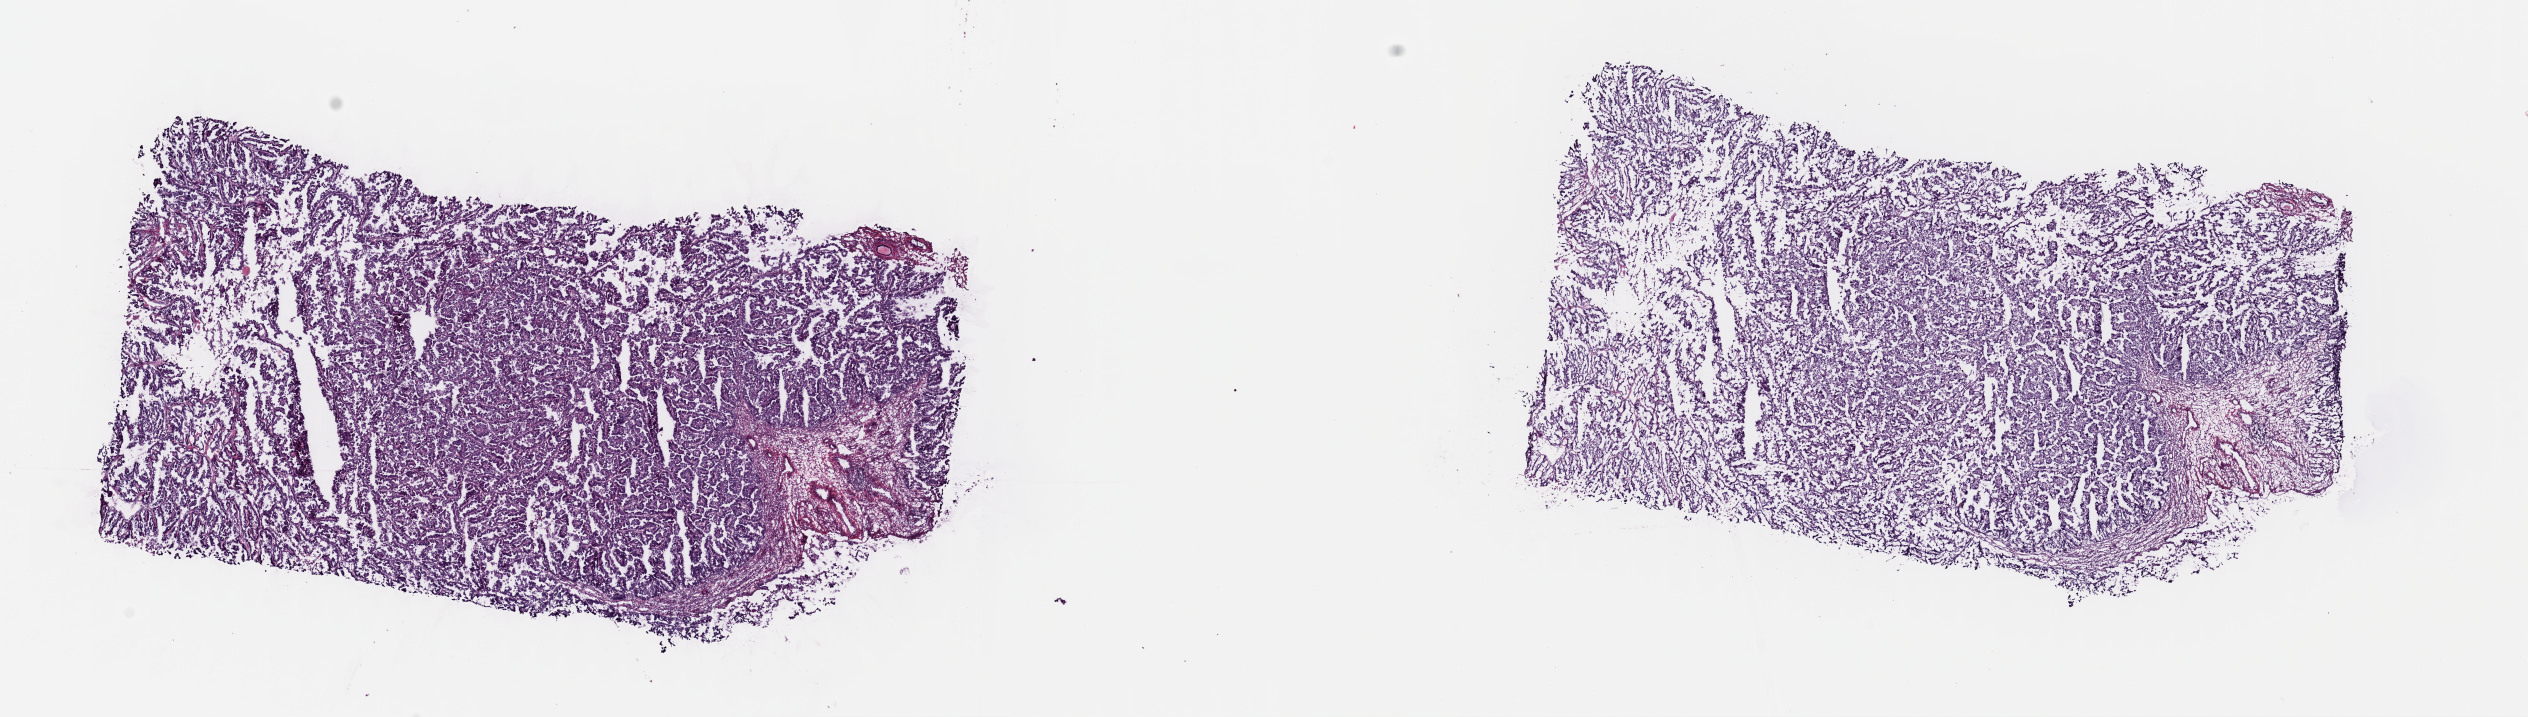
Hematoxylin and eosin (H&E) stained whole-slide image, a low-resolution overview of the entire scanned area, about 20.0 x 5.7 mm. Frozen section. Sample: primary tumour, uterus. Female patient; age at initial diagnosis 65 years. Composition of this section per pathologist review: tumour cells 60%, tumour nuclei 80%.
Diagnosis: Serous cystadenocarcinoma, NOS (endometrium).